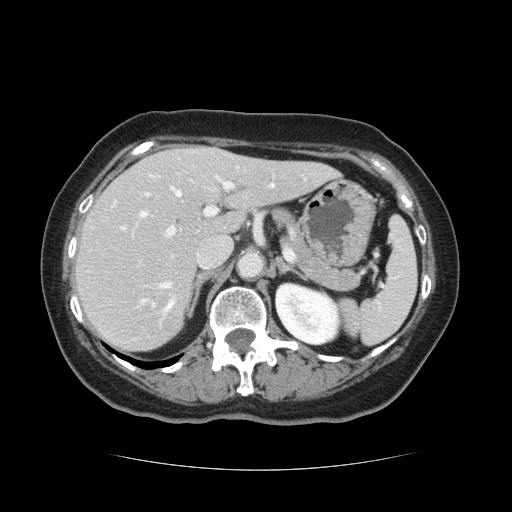
Contrast-enhanced abdominal CT, one axial slice; slice 77 of 128 in the series (ordered by position); soft-tissue window (W 400 / L 40 HU); 2.5 mm slice thickness; 512 × 512 image matrix, field of view 366 × 366 mm. Female patient, age 67 years. From the clinical record (not read from this slice): diagnosis: colorectal cancer liver metastases, imaged before liver resection; multiple liver metastases: yes; largest metastasis: 3 cm.
Structures marked on this image (expert manual segmentation):
- hepatic veins: bounding box <140,185,274,314> (left, top, right, bottom; pixels)
- liver: <74,146,335,351>
- planned liver remnant (the part of the liver to remain after resection): <75,158,335,351>
- portal vein (with intrahepatic branches): <120,174,235,307>